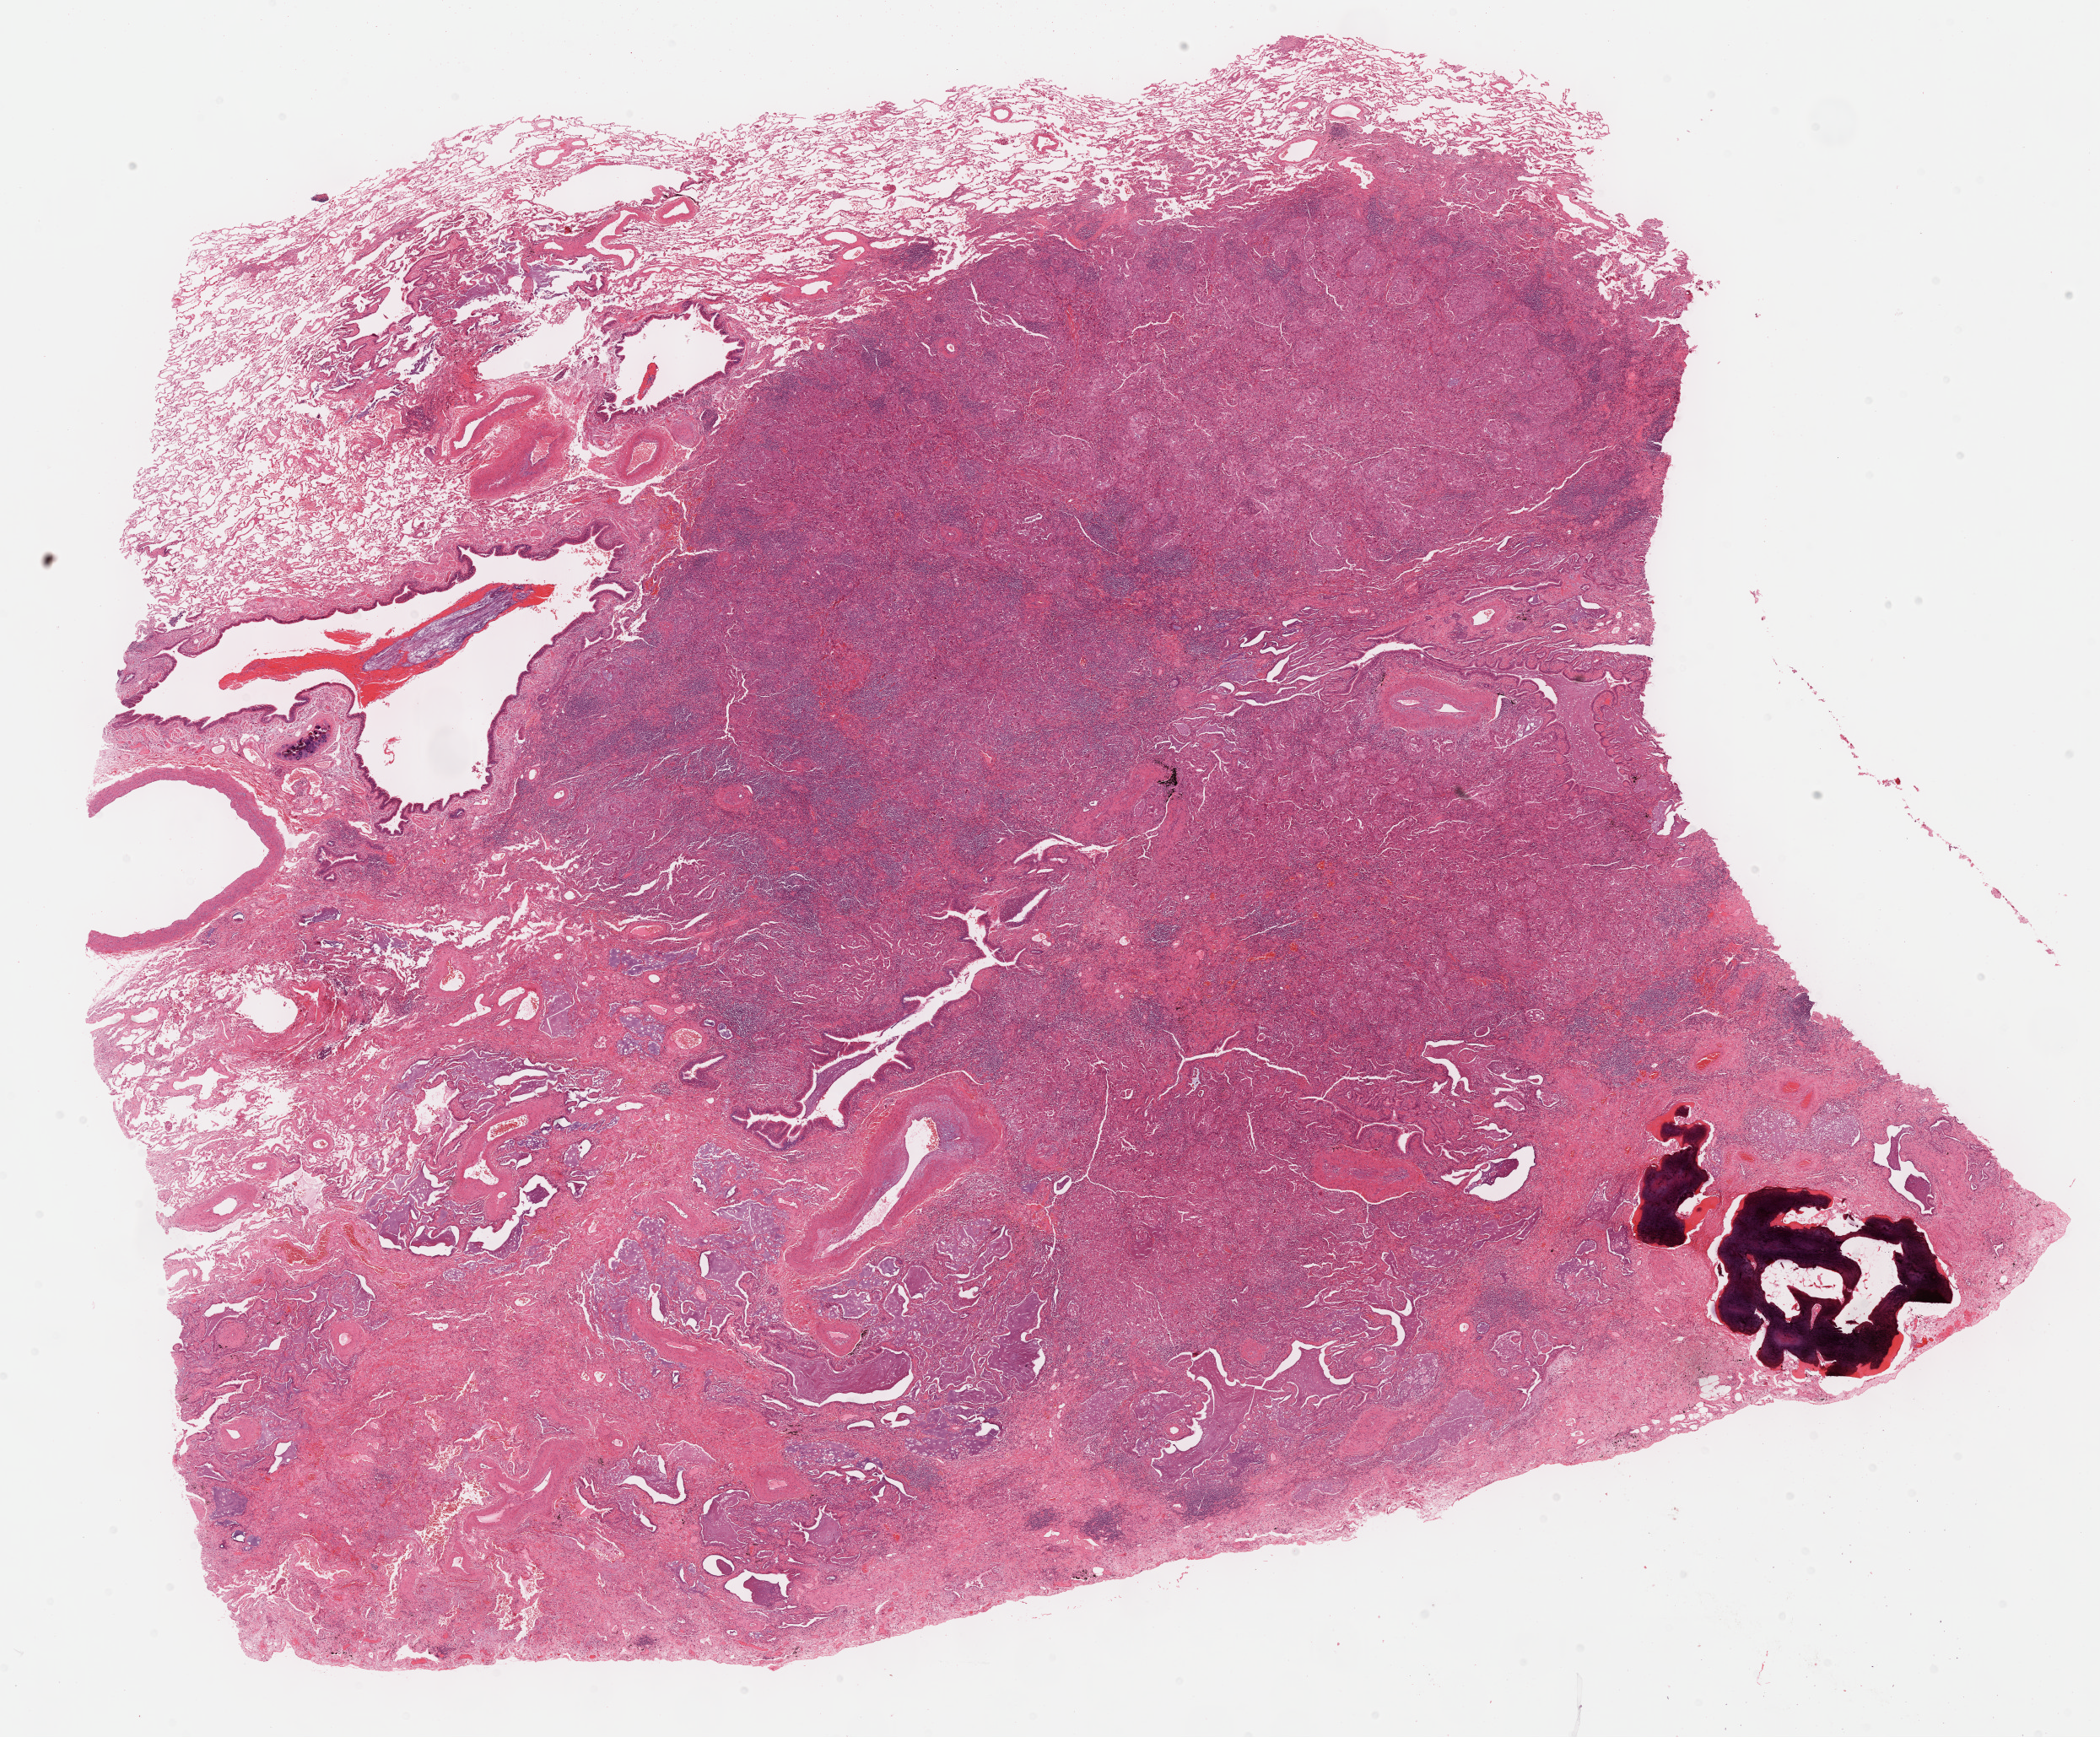
Digitized Hematoxylin and eosin (H&E) stained tissue section (whole slide) — low-resolution overview of the scanned area, about 20.1 x 16.7 mm, formalin-fixed paraffin-embedded (FFPE) diagnostic section, lung, primary tumour sample. Male patient; age at initial diagnosis 70 years.
Laterality: right. Diagnosis: Adenocarcinoma with mixed subtypes. AJCC pathologic stage: IA (7th edition).